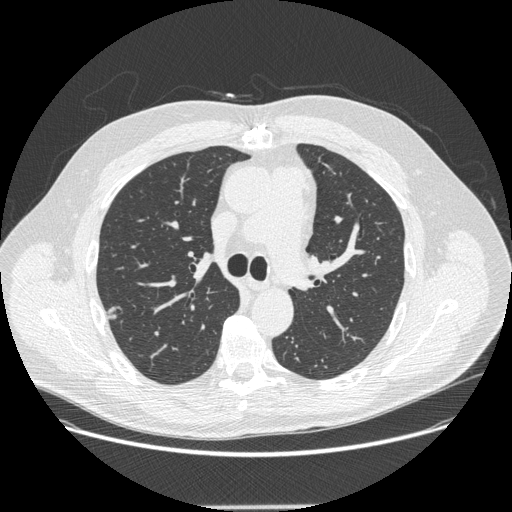
Low-dose screening chest CT, one axial slice. Slice 185 of 265 in the series (ordered by position). Reconstruction kernel STANDARD. 120 kVp. Lung window (W 1500 / L -600 HU). 1.25 mm slice thickness. 512 × 512 image matrix, field of view 400 × 400 mm.
Outlined on this slice (expert manual segmentation):
- lesion 1 (tumor, upper lobe of right lung): bounding box <108,306,123,319> (left, top, right, bottom; pixels)